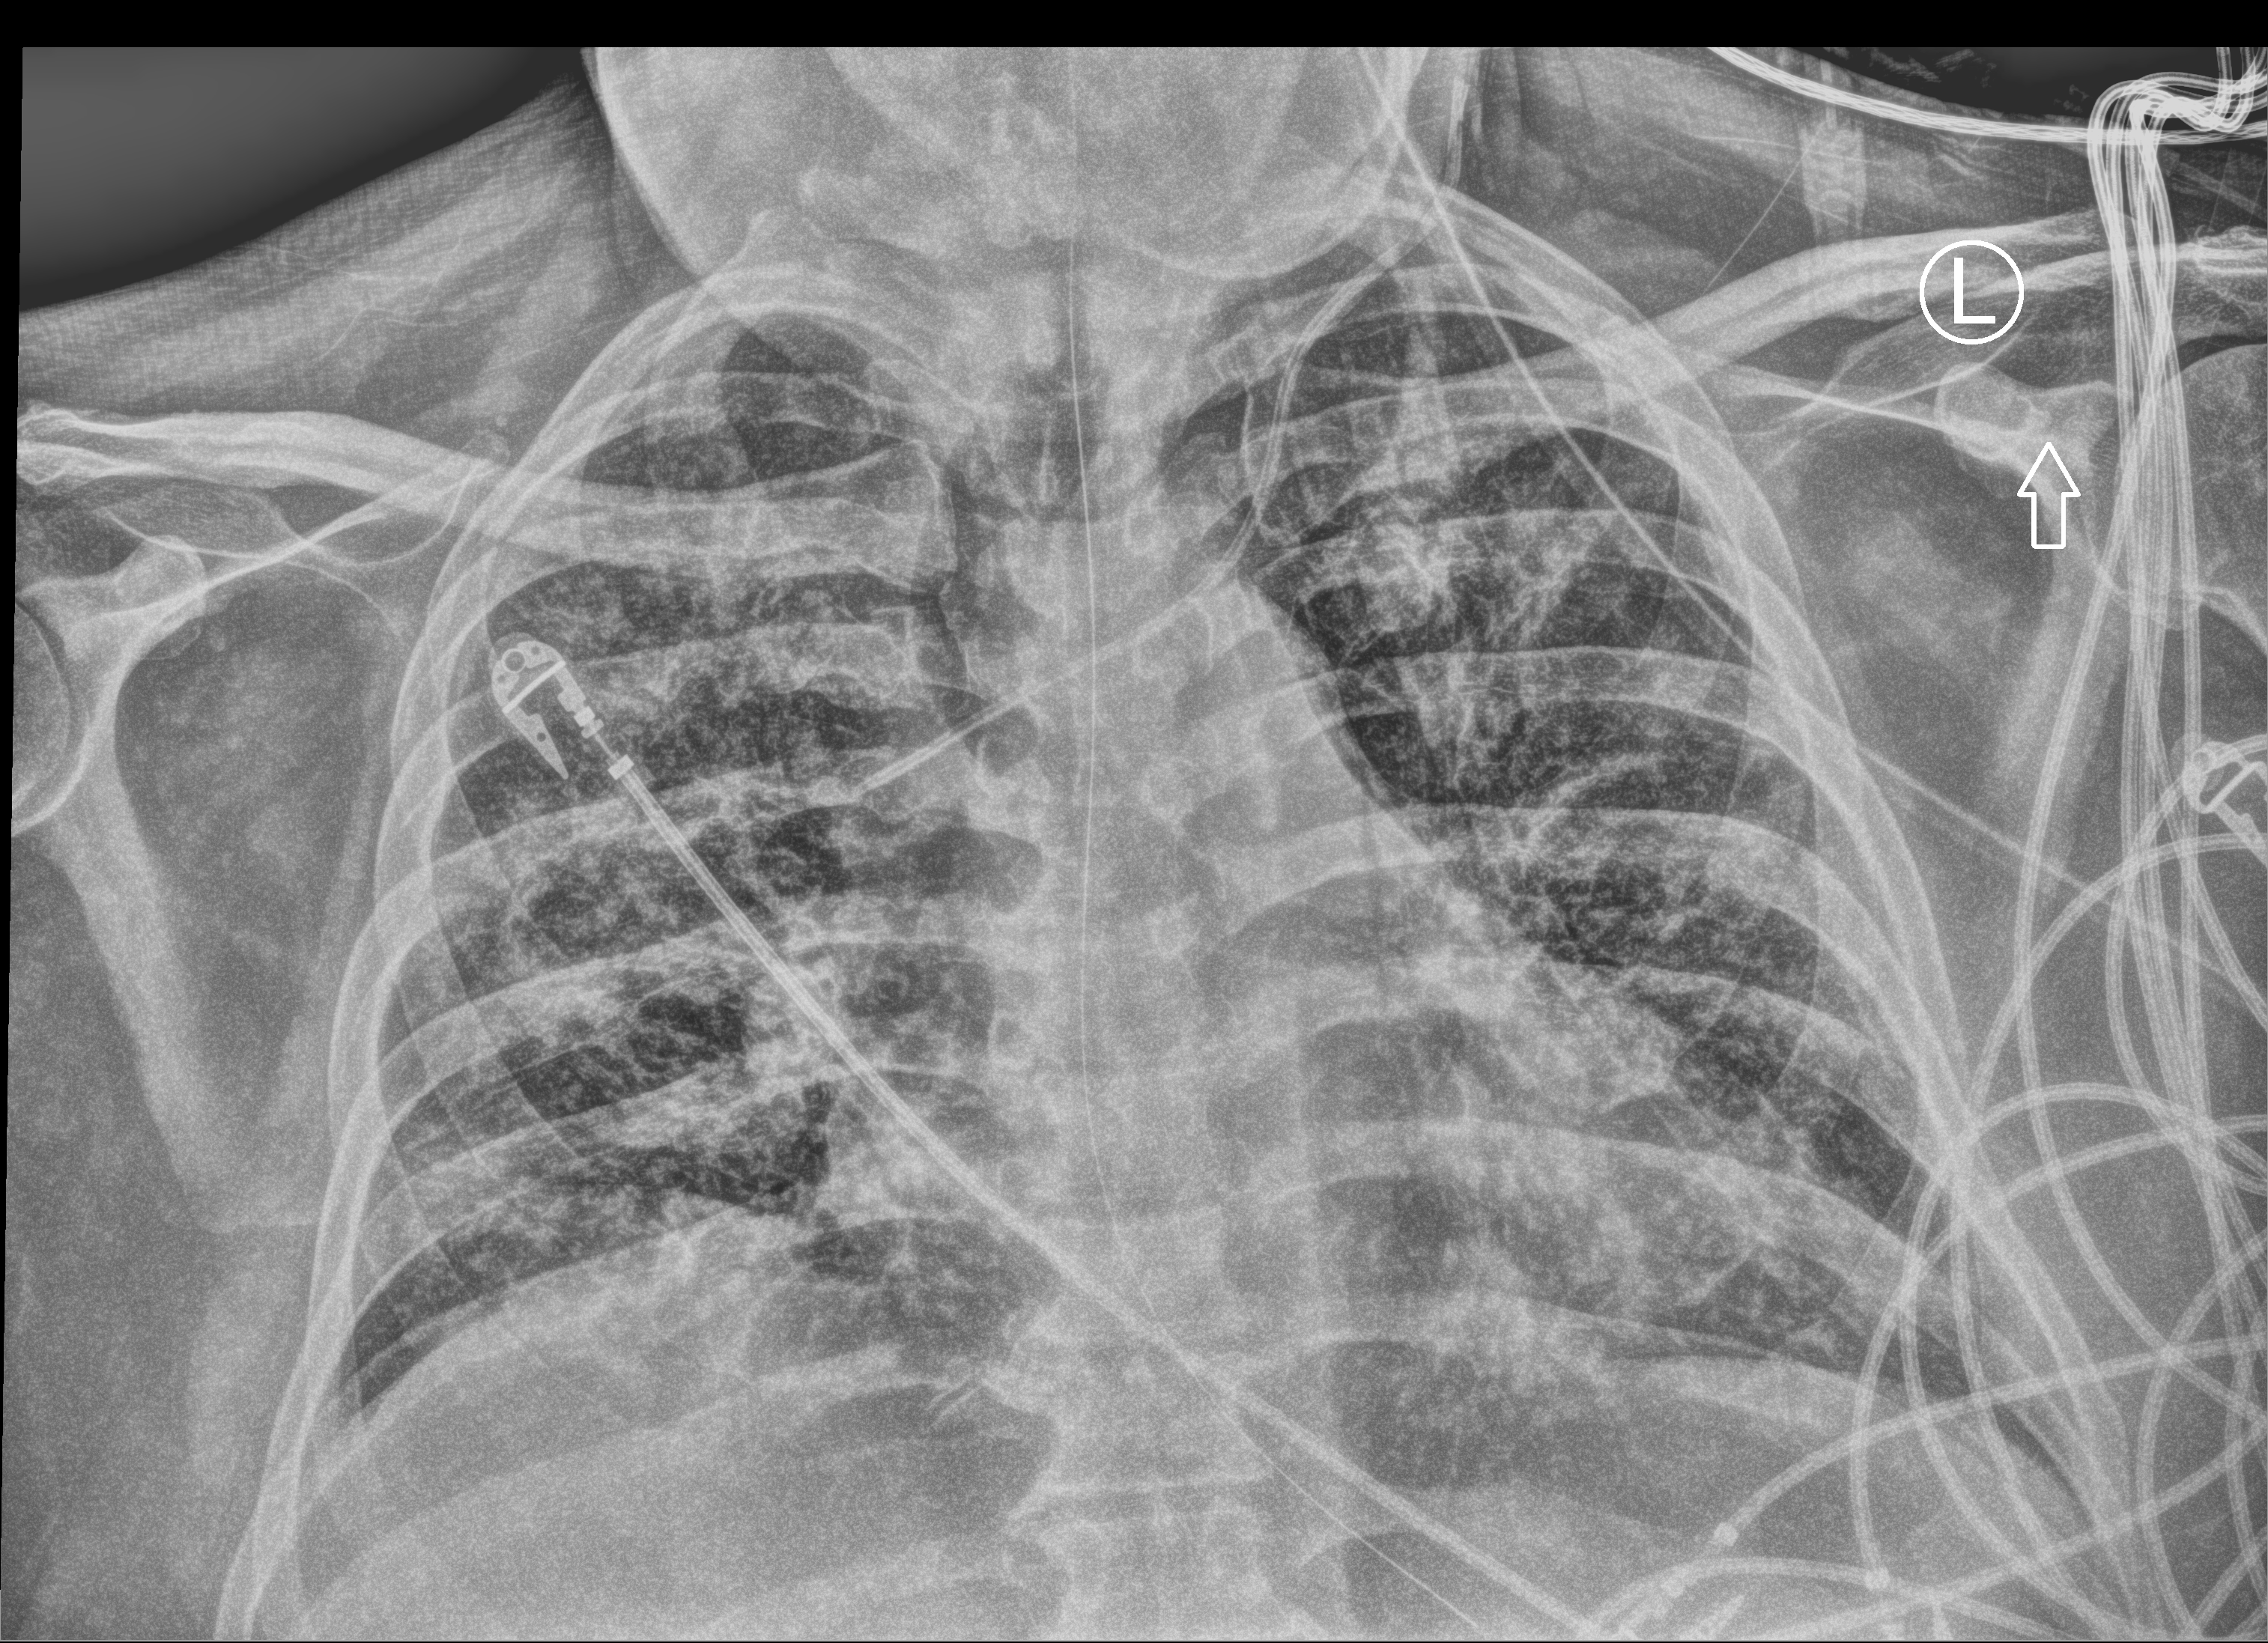
Chest X-ray (portable); anteroposterior (AP) projection. Male patient hospitalised with COVID-19, age 18–59 years.
From the hospital-stay record, not from the radiograph (when in the stay this image was taken is not recorded): mechanically ventilated during this hospital stay: yes; admitted to intensive care during this hospital stay: yes.